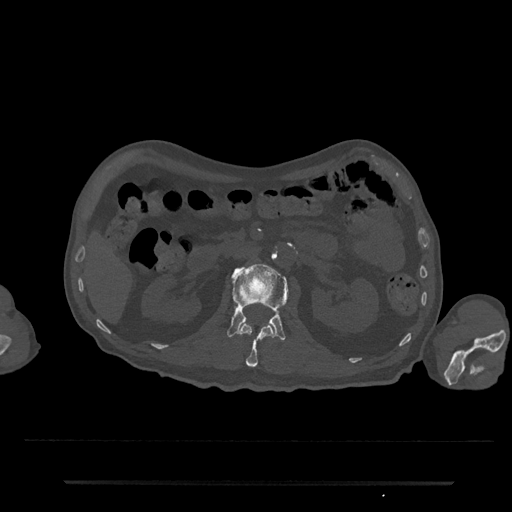
CT including the spine, one axial slice. Position 91 of 797 along the scan axis. Bone window (W 1800 / L 400 HU). 0.5 mm slice thickness. 512 × 512 image matrix, field of view 427 × 427 mm. Patient: male, 74 years. Case-level facts recorded for this patient, not image findings: primary cancer: prostate.
Outlined on this slice (semi-automatically segmented with operator editing):
- L1 vertebra: bounding box [x1, y1, x2, y2] px = [238, 323, 274, 367]
- L2 vertebra: [227, 263, 288, 341]